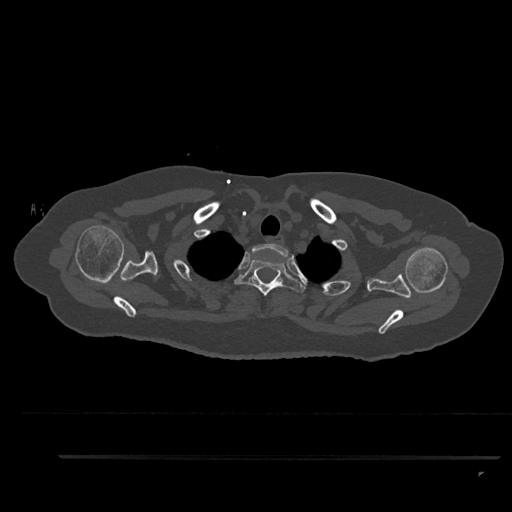
CT including the spine, one axial slice. 120 kVp. Bone window (W 1800 / L 400 HU). 512 × 512 image matrix, field of view 408 × 408 mm. Patient: female, 44 years. Case-level facts recorded for this patient, not image findings: primary cancer: renal; vertebrae with lytic lesions (as recorded): L1.
Outlined on this slice (semi-automatically segmented with operator editing):
- T1 vertebra: bounding box (x1, y1, x2, y2) in pixels: (250, 244, 289, 260)
- T2 vertebra: (234, 258, 306, 296)